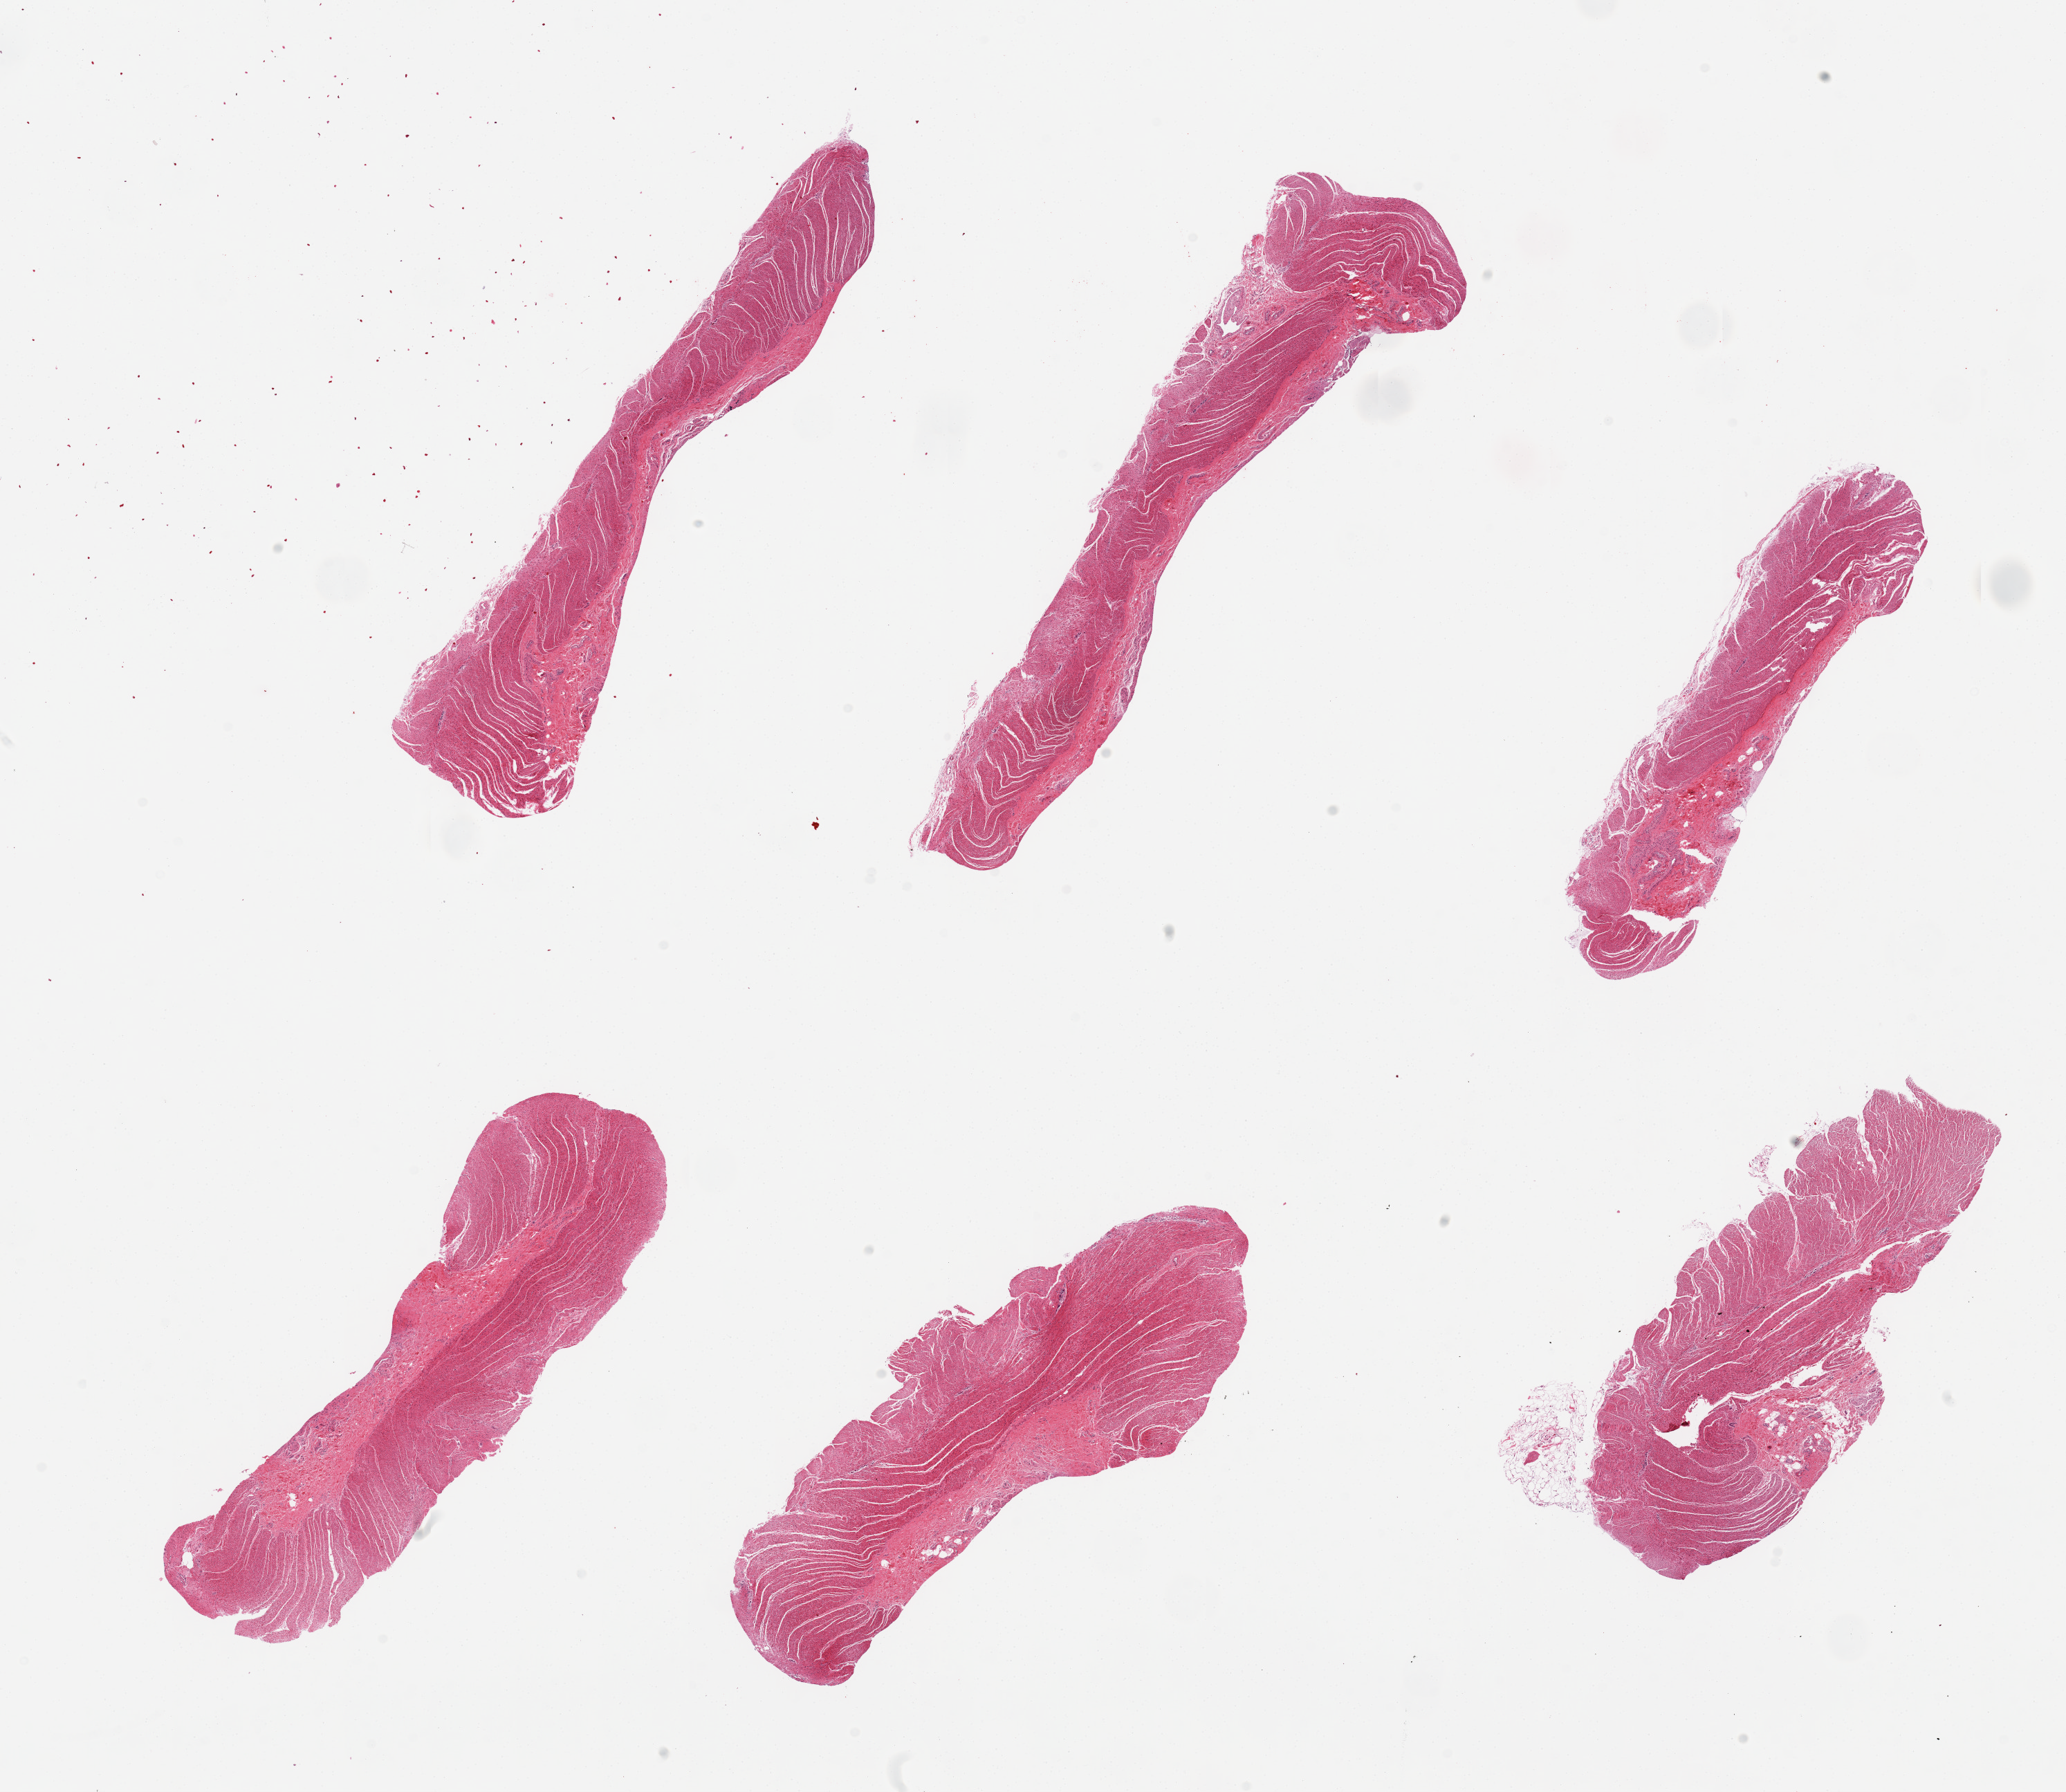
Whole-slide image, haematoxylin and eosin stain, low-resolution overview of the scanned area, about 23.6 x 20.5 mm (slide scanned at 20x), PAXgene-fixed, paraffin-embedded tissue, sampled site (target tissue): sigmoid colon, tissue donor sample. Donor sex: male.
• pathologist's review note for this sample: 6 pieces, all muscularis, good specimens